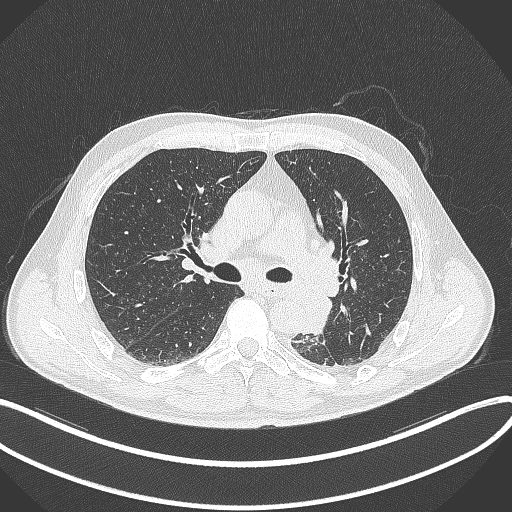
Chest CT, one axial slice. Position 210 of 329 along the scan axis. Reconstruction kernel B70f. 120 kVp. Lung window (W 1500 / L -600 HU). 1 mm slice thickness. 512 × 512 image matrix. Patient: male, 59 years. From the clinical record (not read from this slice): clinical TNM (as recorded): T2a N2 M0.
Structures marked on this image (rectangle marked by the reading radiologist):
- lung tumour (recorded histology: squamous cell carcinoma): bounding box [x1, y1, x2, y2] px = [300, 288, 337, 340]